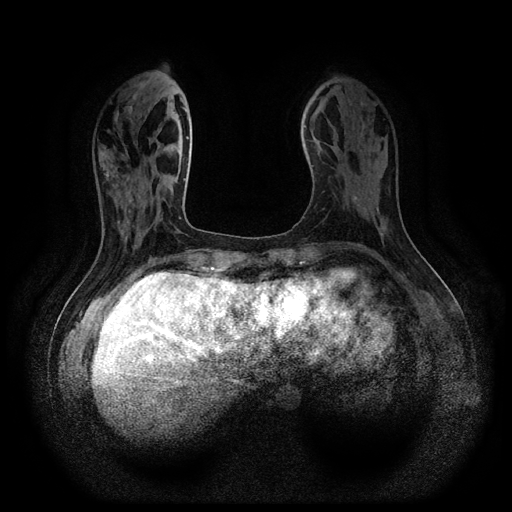
Breast MRI (dynamic contrast-enhanced, multi-phase), one axial slice. Slice 33 of 116 in the series (ordered by position). Dynamic contrast-enhanced series, time point 2 of 5 at this slice position (early post-contrast). 1.5 T. TE 2.6 ms, TR 5.3 ms. 2.2 mm slice thickness. 512 × 512 image matrix, field of view 340 × 340 mm. Patient: female, 54 years.
Annotated regions visible in this slice (semi-automatic segmentation, software-assisted and operator-edited):
- breast lesion (labelled benign in the annotation): bounding box <352,195,359,206> (left, top, right, bottom; pixels)